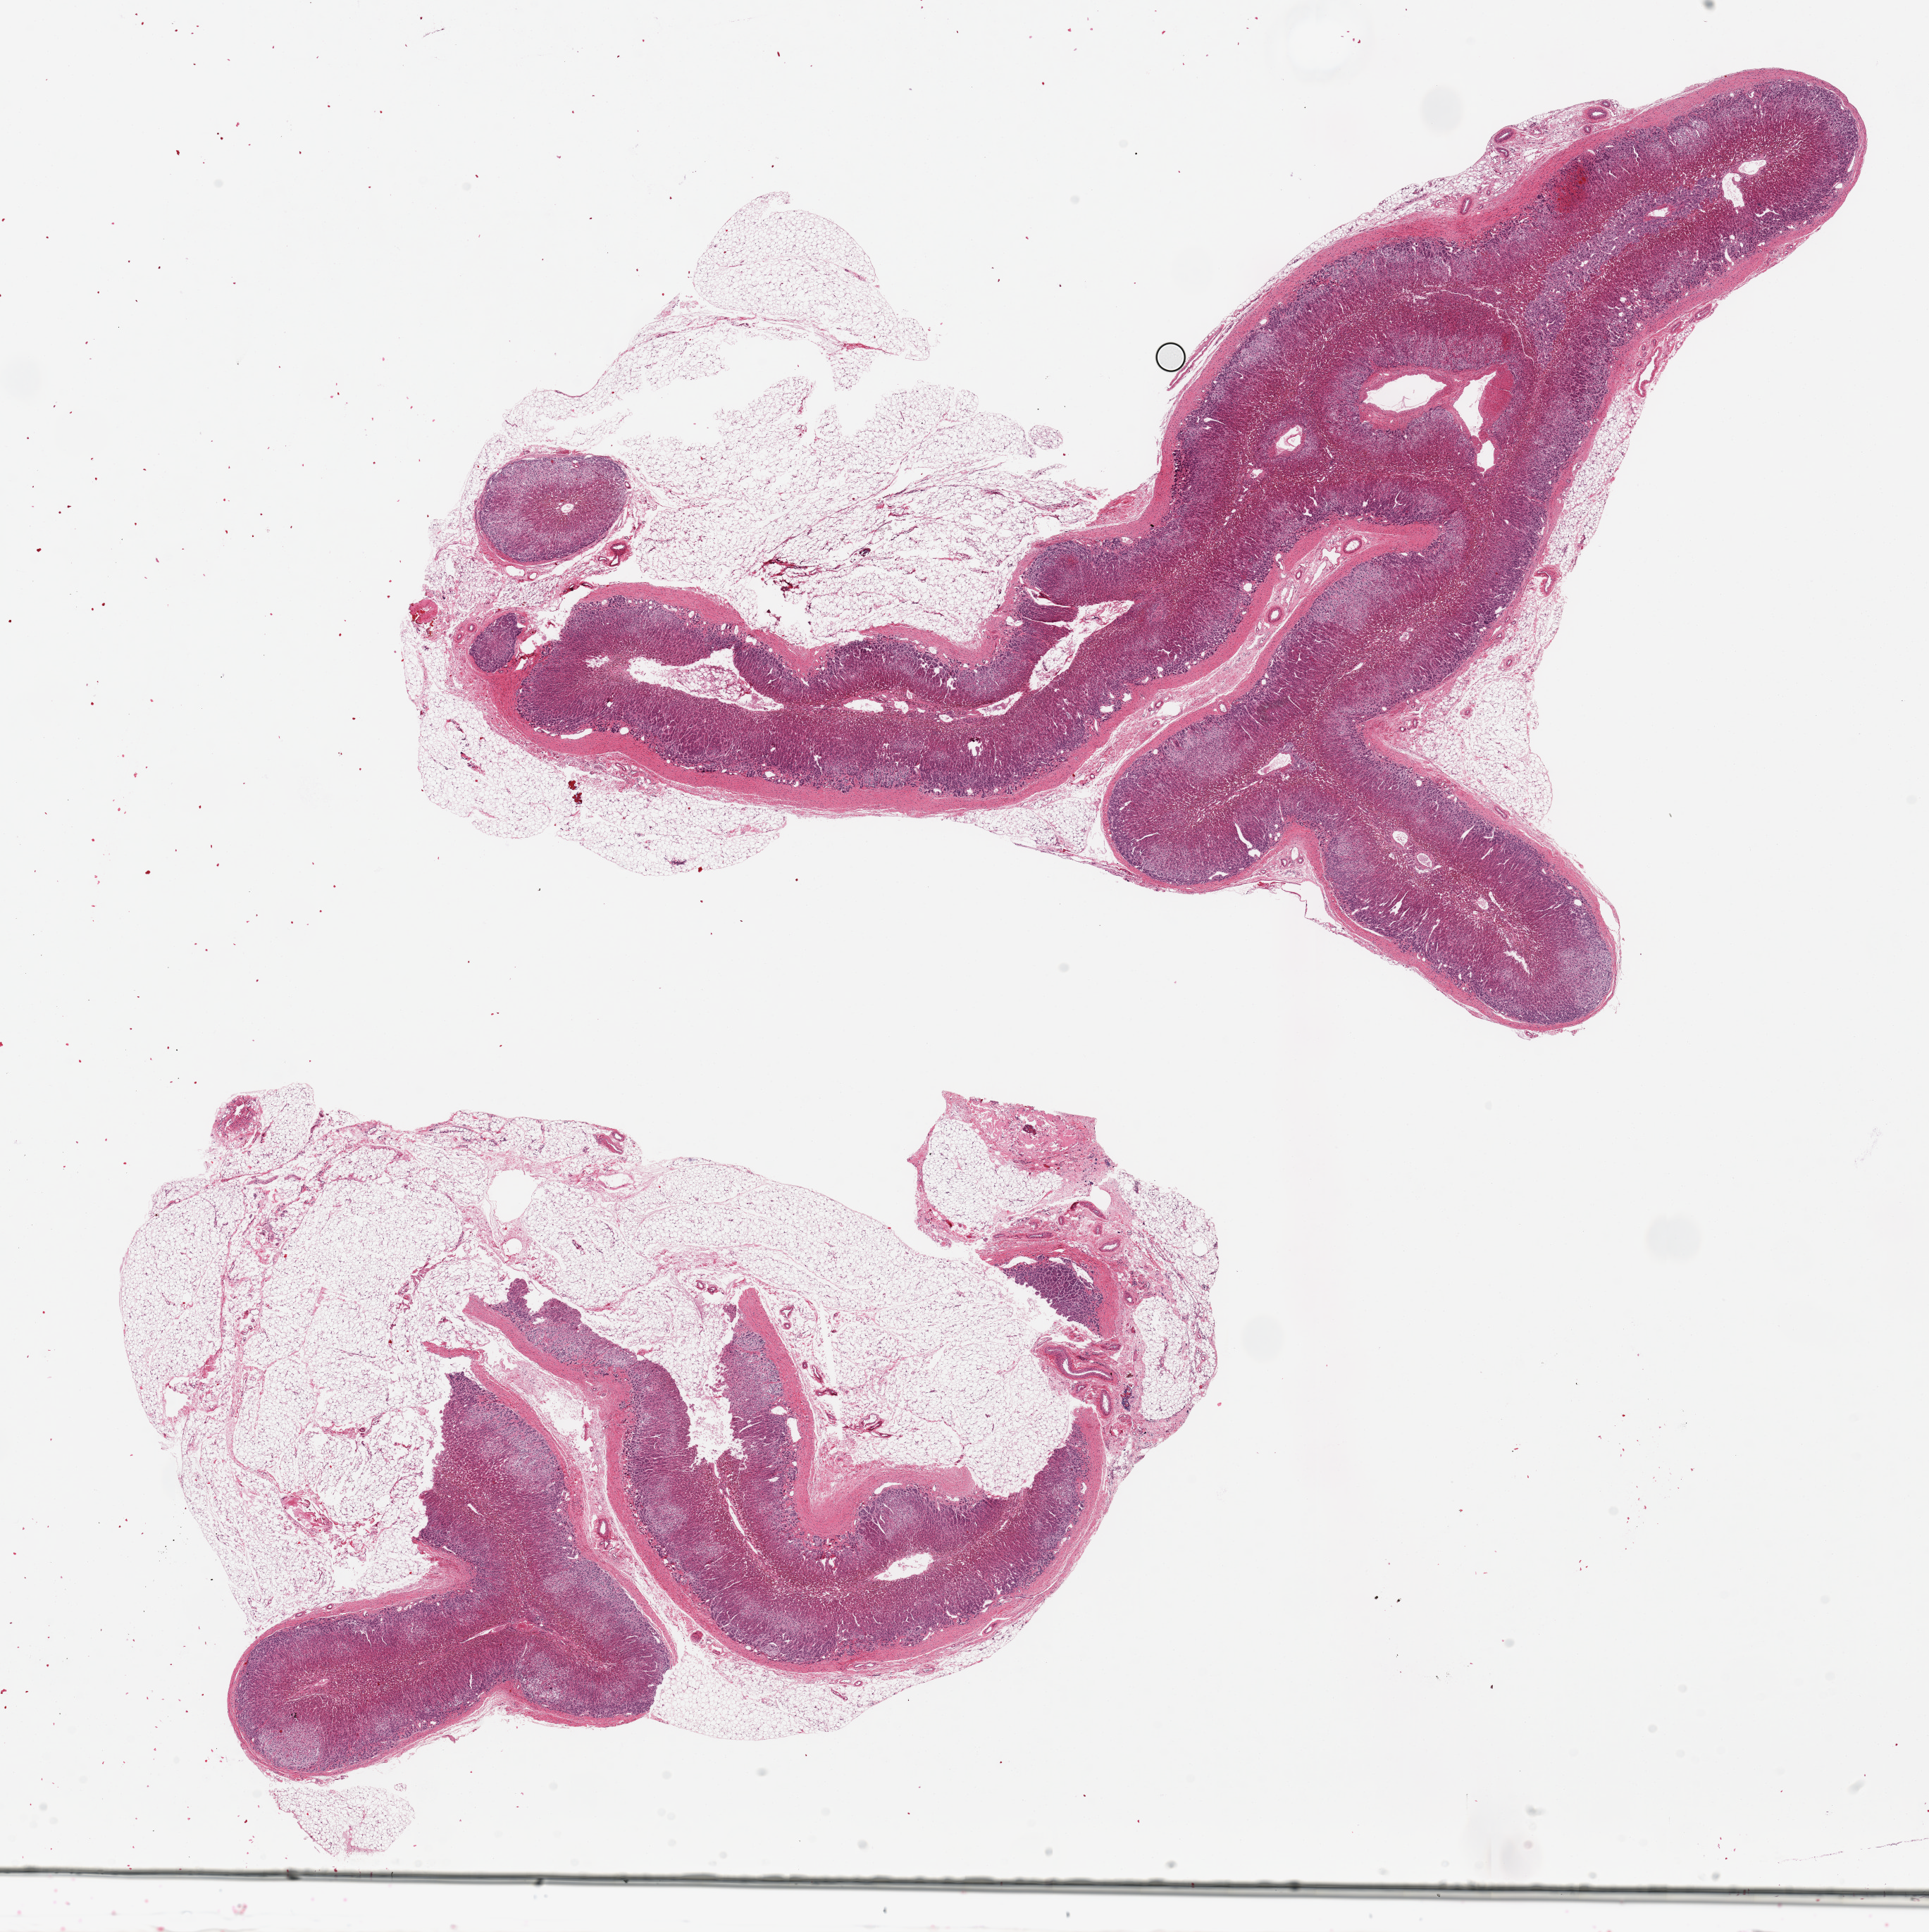
Whole-slide image, haematoxylin and eosin stain — shown as a low-resolution overview of the whole scanned area (about 21.7 x 21.7 mm, acquisition: 20x scan), PAXgene-fixed paraffin-embedded (PFPE) section, section of adrenal gland (target tissue), donor tissue sample. Donor: female.
Review note (as recorded): 2 pieces ~12x11mm, adherent fat up to~40/50% of both aliquots which are irreuglarly shaped.